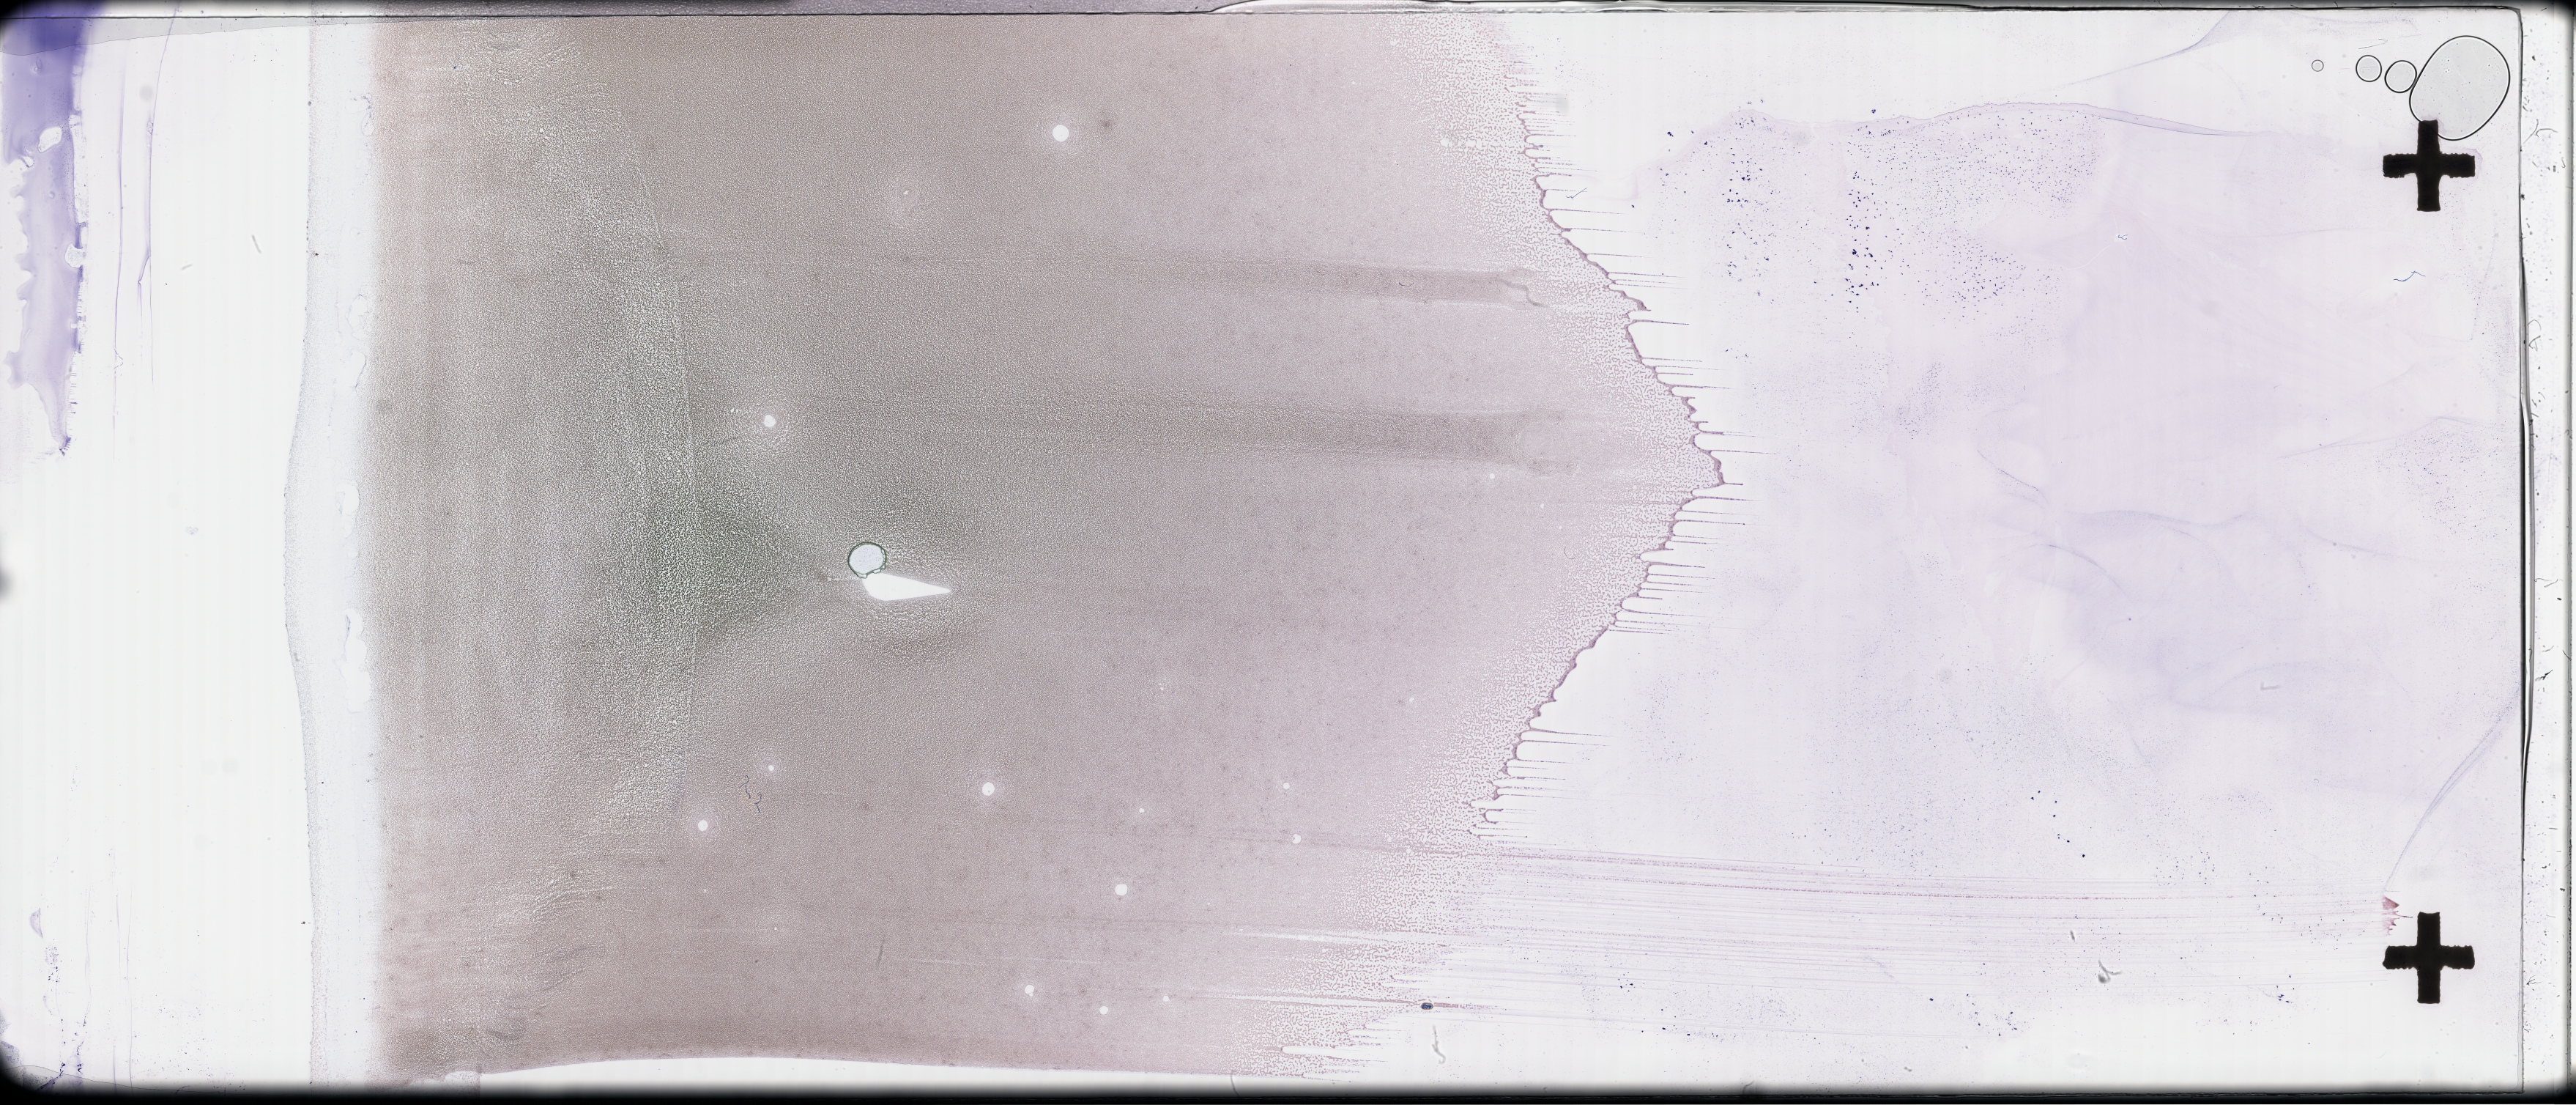
Whole-slide image of a whole blood smear, Wright–Giemsa stain, a low-resolution overview of the entire scanned area, about 56.8 x 24.4 mm. EDTA-anticoagulated smear. Collected at disease progression. Female patient.
Patient diagnosis: Plasma Cell Myeloma.